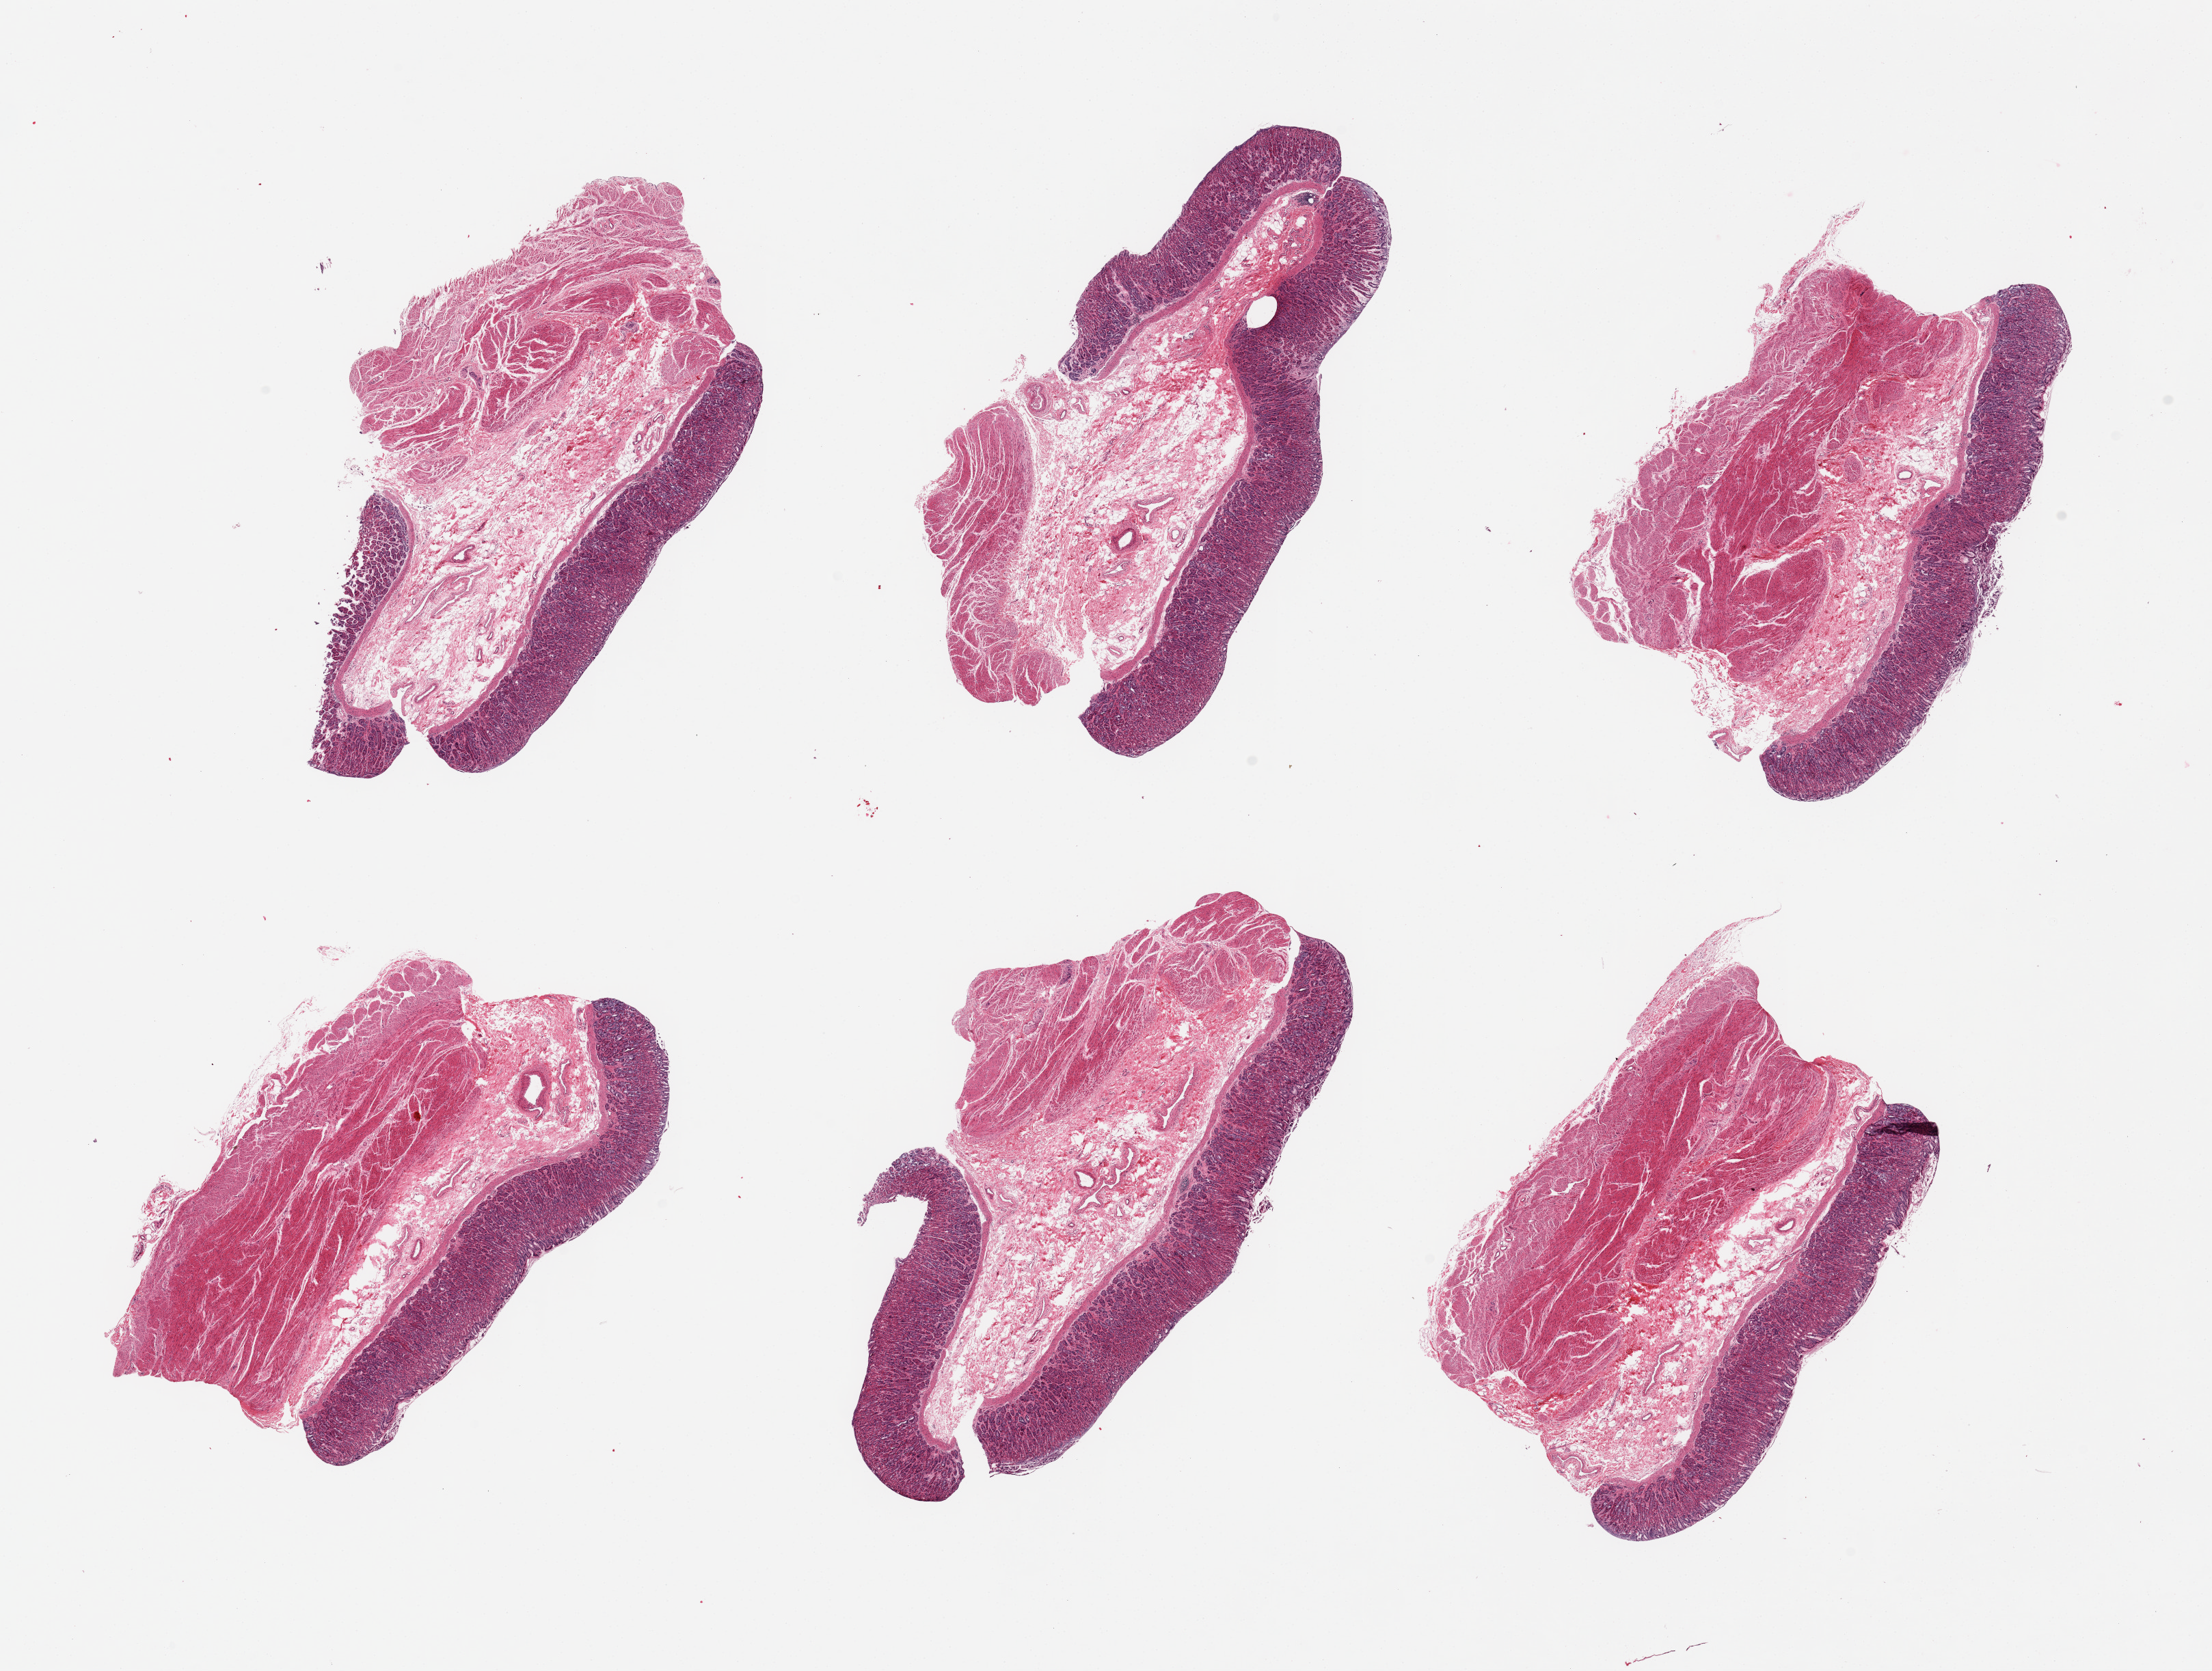
Digitized H&E-stained section — a low-resolution overview of the entire scanned area, about 25.6 x 19.3 mm; PAXgene-fixed paraffin-embedded (PFPE) section; sampled site (target tissue): stomach; donor tissue sample. Donor: male.
Review note (as recorded): 6 pieces, mucosa (2), muscularis (1).